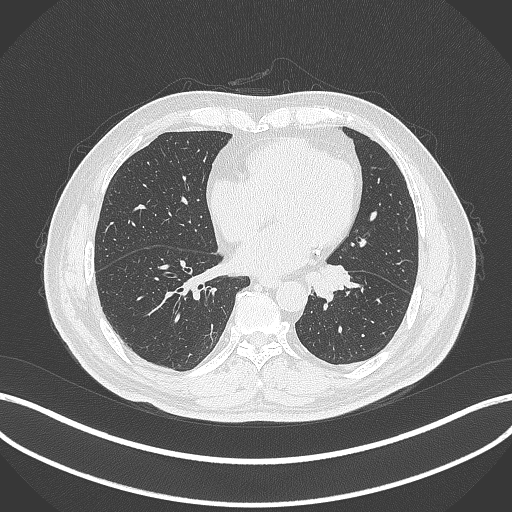
Chest CT, one axial slice; reconstruction kernel B70f; lung window (W 1500 / L -600 HU); 1 mm slice thickness; 512 × 512 image matrix, field of view 400 × 400 mm. Patient: male, 71 years. From the clinical record (not read from this slice): clinical TNM (as recorded): T1b N0 M0.
Structures marked on this image (bounding box drawn by a radiologist):
- lung tumour (recorded histology: squamous cell carcinoma): box from (x=303, y=261) to (x=359, y=300) px